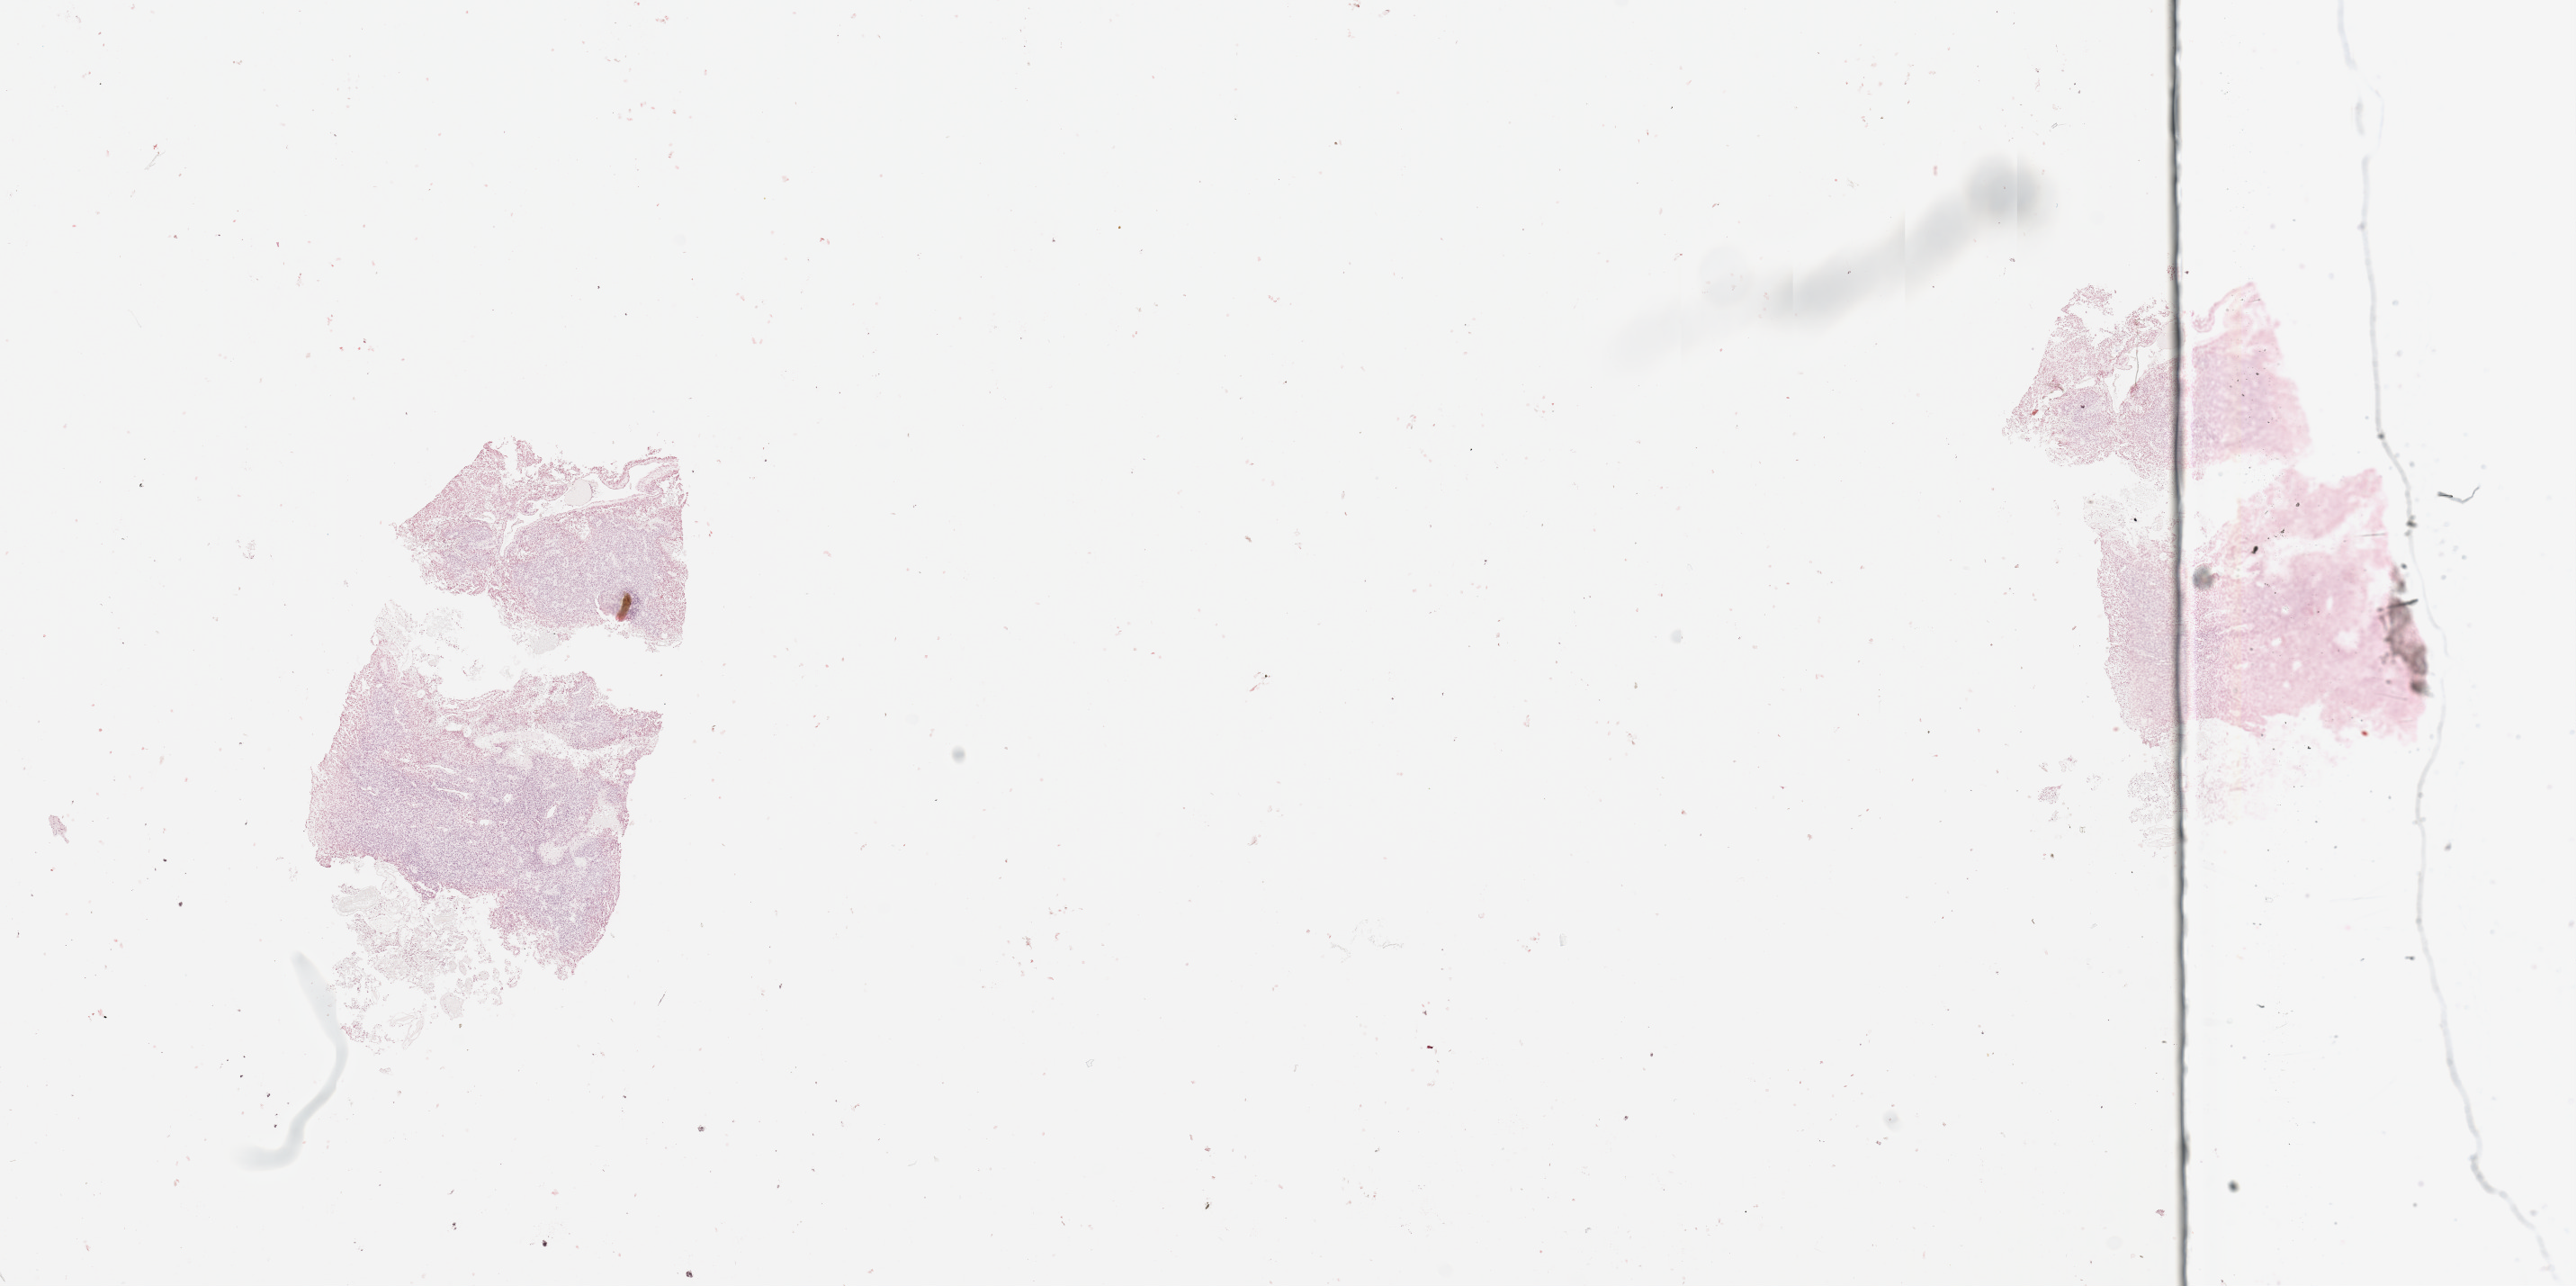
Whole-slide histology image, H&E — low-resolution overview of the scanned area, about 22.6 x 11.3 mm; tumour tissue sample, sampled site: frontal lobe. Patient: male, age 59 years. Composition of this section per pathologist review: tumour nuclei 80%, necrosis 5%.
Diagnosis: Glioblastoma. Primary tumour site (as recorded): frontal lobe.